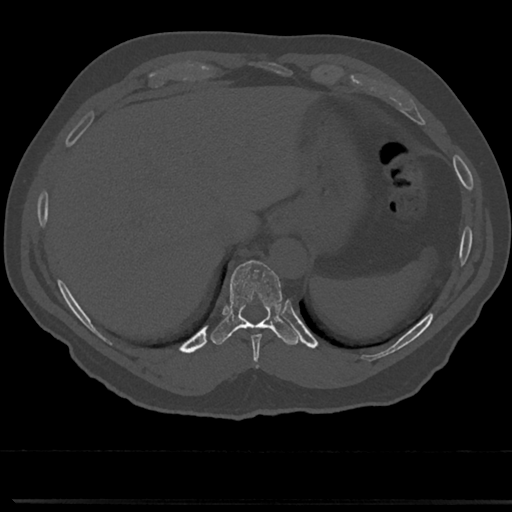
CT including the spine, one axial slice; position 267 of 817 along the scan axis; bone window (W 1800 / L 400 HU); 0.5 mm slice thickness; 512 × 512 image matrix, field of view 355 × 355 mm. Male patient, age 61 years. Case-level facts recorded for this patient, not image findings: primary cancer: prostate.
Structures marked on this image (semi-automatically segmented with operator editing):
- T10 vertebra: bounding box <229,261,283,325> (left, top, right, bottom; pixels)
- T9 vertebra: <238,322,278,354>